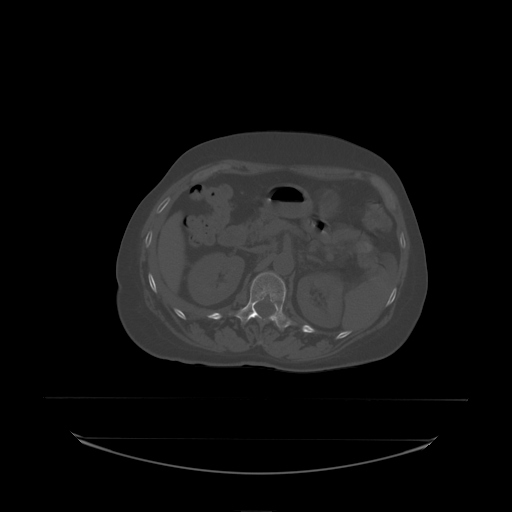
CT including the spine, one axial slice; slice 85 of 242 in the series (ordered by position); bone window (W 1800 / L 400 HU); 512 × 512 image matrix, field of view 500 × 500 mm. Female patient, age 53 years. From the clinical record (not read from this slice): primary cancer: lung; vertebrae with lytic lesions (as recorded): T7, L1.
Structures marked on this image (semi-automatically segmented with operator editing):
- L1 vertebra: bounding box [x1, y1, x2, y2] px = [236, 272, 292, 330]